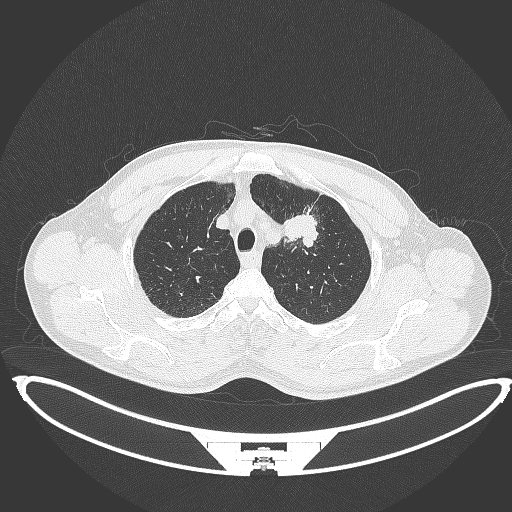
Chest CT, one axial slice; reconstruction kernel B70f; 120 kVp; lung window (W 1500 / L -600 HU); 512 × 512 image matrix. Patient: male, 60 years. Case-level facts recorded for this patient, not image findings: clinical TNM (as recorded): T2a N0 M0.
Structures marked on this image (rectangle marked by the reading radiologist):
- lung tumour (recorded histology: squamous cell carcinoma): box from (x=282, y=212) to (x=320, y=251) px